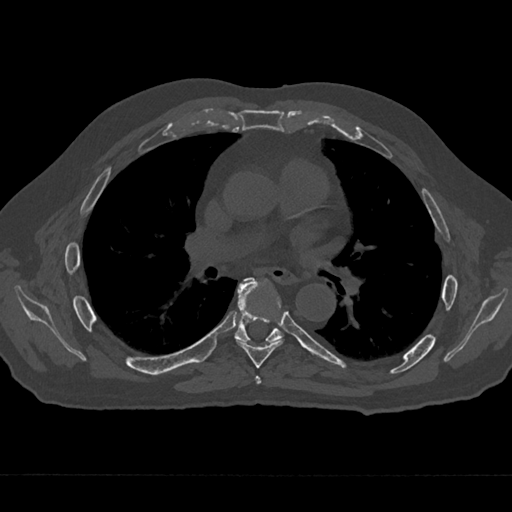
CT including the spine, one axial slice; 120 kVp; bone window (W 1800 / L 400 HU); 0.5 mm slice thickness; 512 × 512 image matrix, field of view 377 × 377 mm. Patient: male, 75 years. From the clinical record (not read from this slice): primary cancer: renal; vertebrae with lytic lesions (as recorded): T4.
Outlined on this slice (semi-automatic segmentation, software-assisted and operator-edited):
- T5 vertebra: bounding box <255,376,261,385> (left, top, right, bottom; pixels)
- T6 vertebra: <236,278,283,368>
- T7 vertebra: <235,278,283,343>